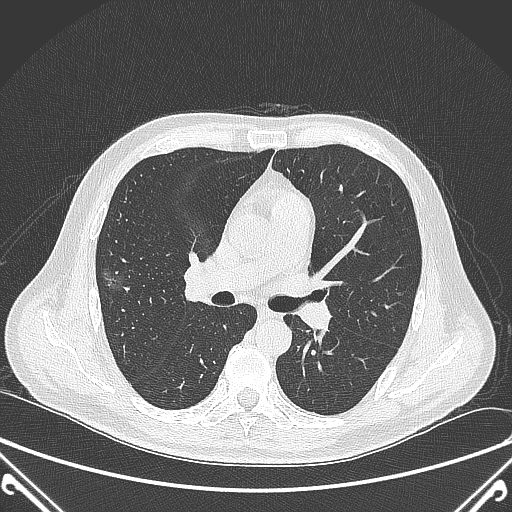
Chest CT, one axial slice. Slice 218 of 360 in the series (ordered by position). 120 kVp. Lung window (W 1500 / L -600 HU). 1 mm slice thickness. 512 × 512 image matrix. Patient: male, 64 years. From the clinical record (not read from this slice): clinical TNM (as recorded): T1c N0 M0.
Outlined on this slice (rectangle marked by the reading radiologist):
- lung tumour (recorded histology: adenocarcinoma): box from (x=101, y=267) to (x=134, y=295) px